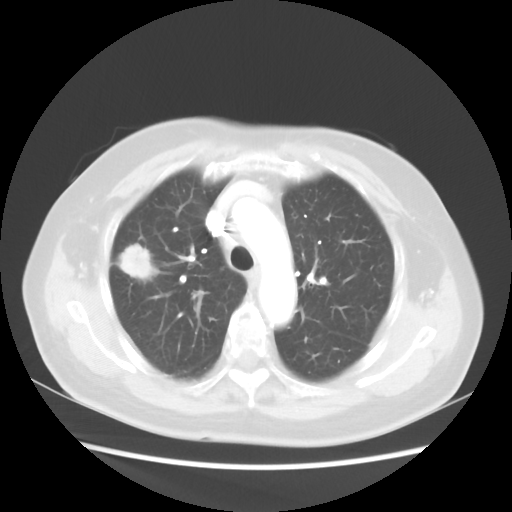
Chest CT, one axial slice; position 34 of 48 along the scan axis; reconstruction kernel STANDARD; 100 kVp; lung window (W 1500 / L -600 HU); 5 mm slice thickness; 512 × 512 image matrix, field of view 360 × 360 mm. Female patient, age 75 years. From the clinical record (not read from this slice): clinical TNM (as recorded): T1c N0 M0.
Annotated regions visible in this slice (rectangle marked by the reading radiologist):
- lung tumour (recorded histology: adenocarcinoma): bounding box <111,238,160,289> (left, top, right, bottom; pixels)